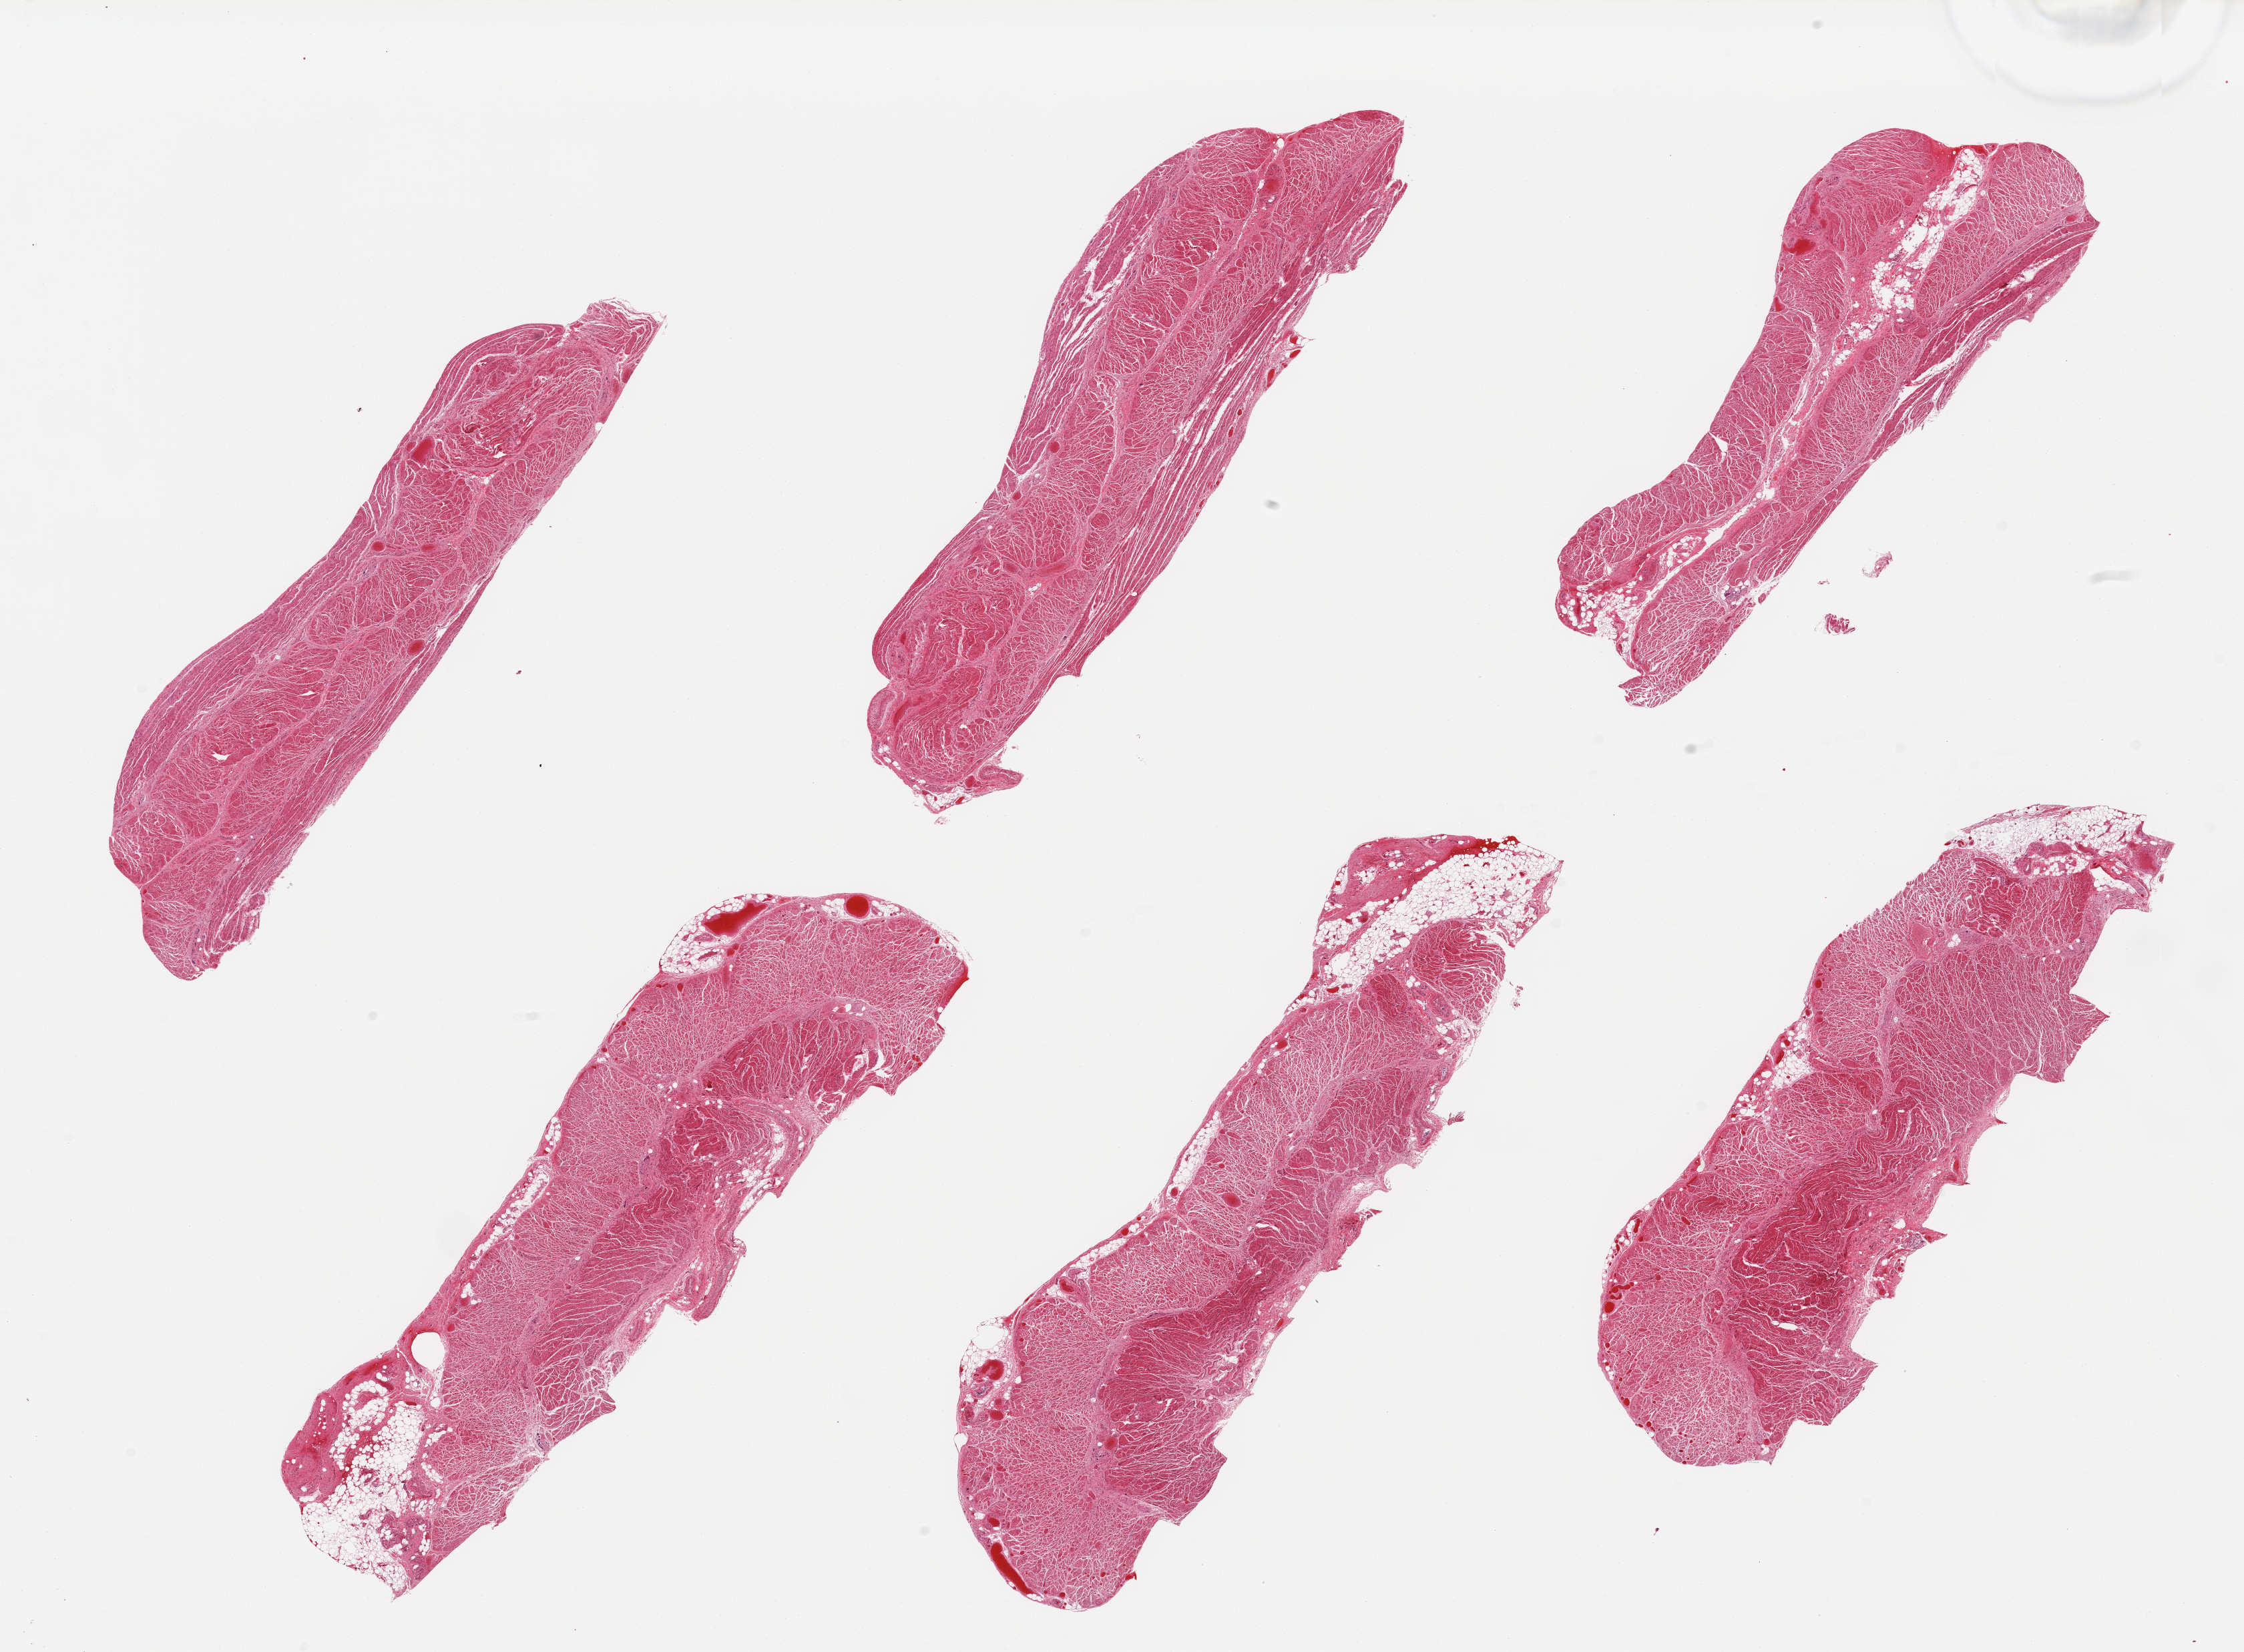
Haematoxylin and eosin whole-slide image, brightfield, a low-resolution overview of the entire scanned area, about 26.6 x 19.6 mm; PAXgene-fixed, paraffin-embedded tissue; section of gastroesophageal junction (target tissue); donor tissue sample.
* review note (as recorded): 6 pieces, good muscularis, trace adherent fat